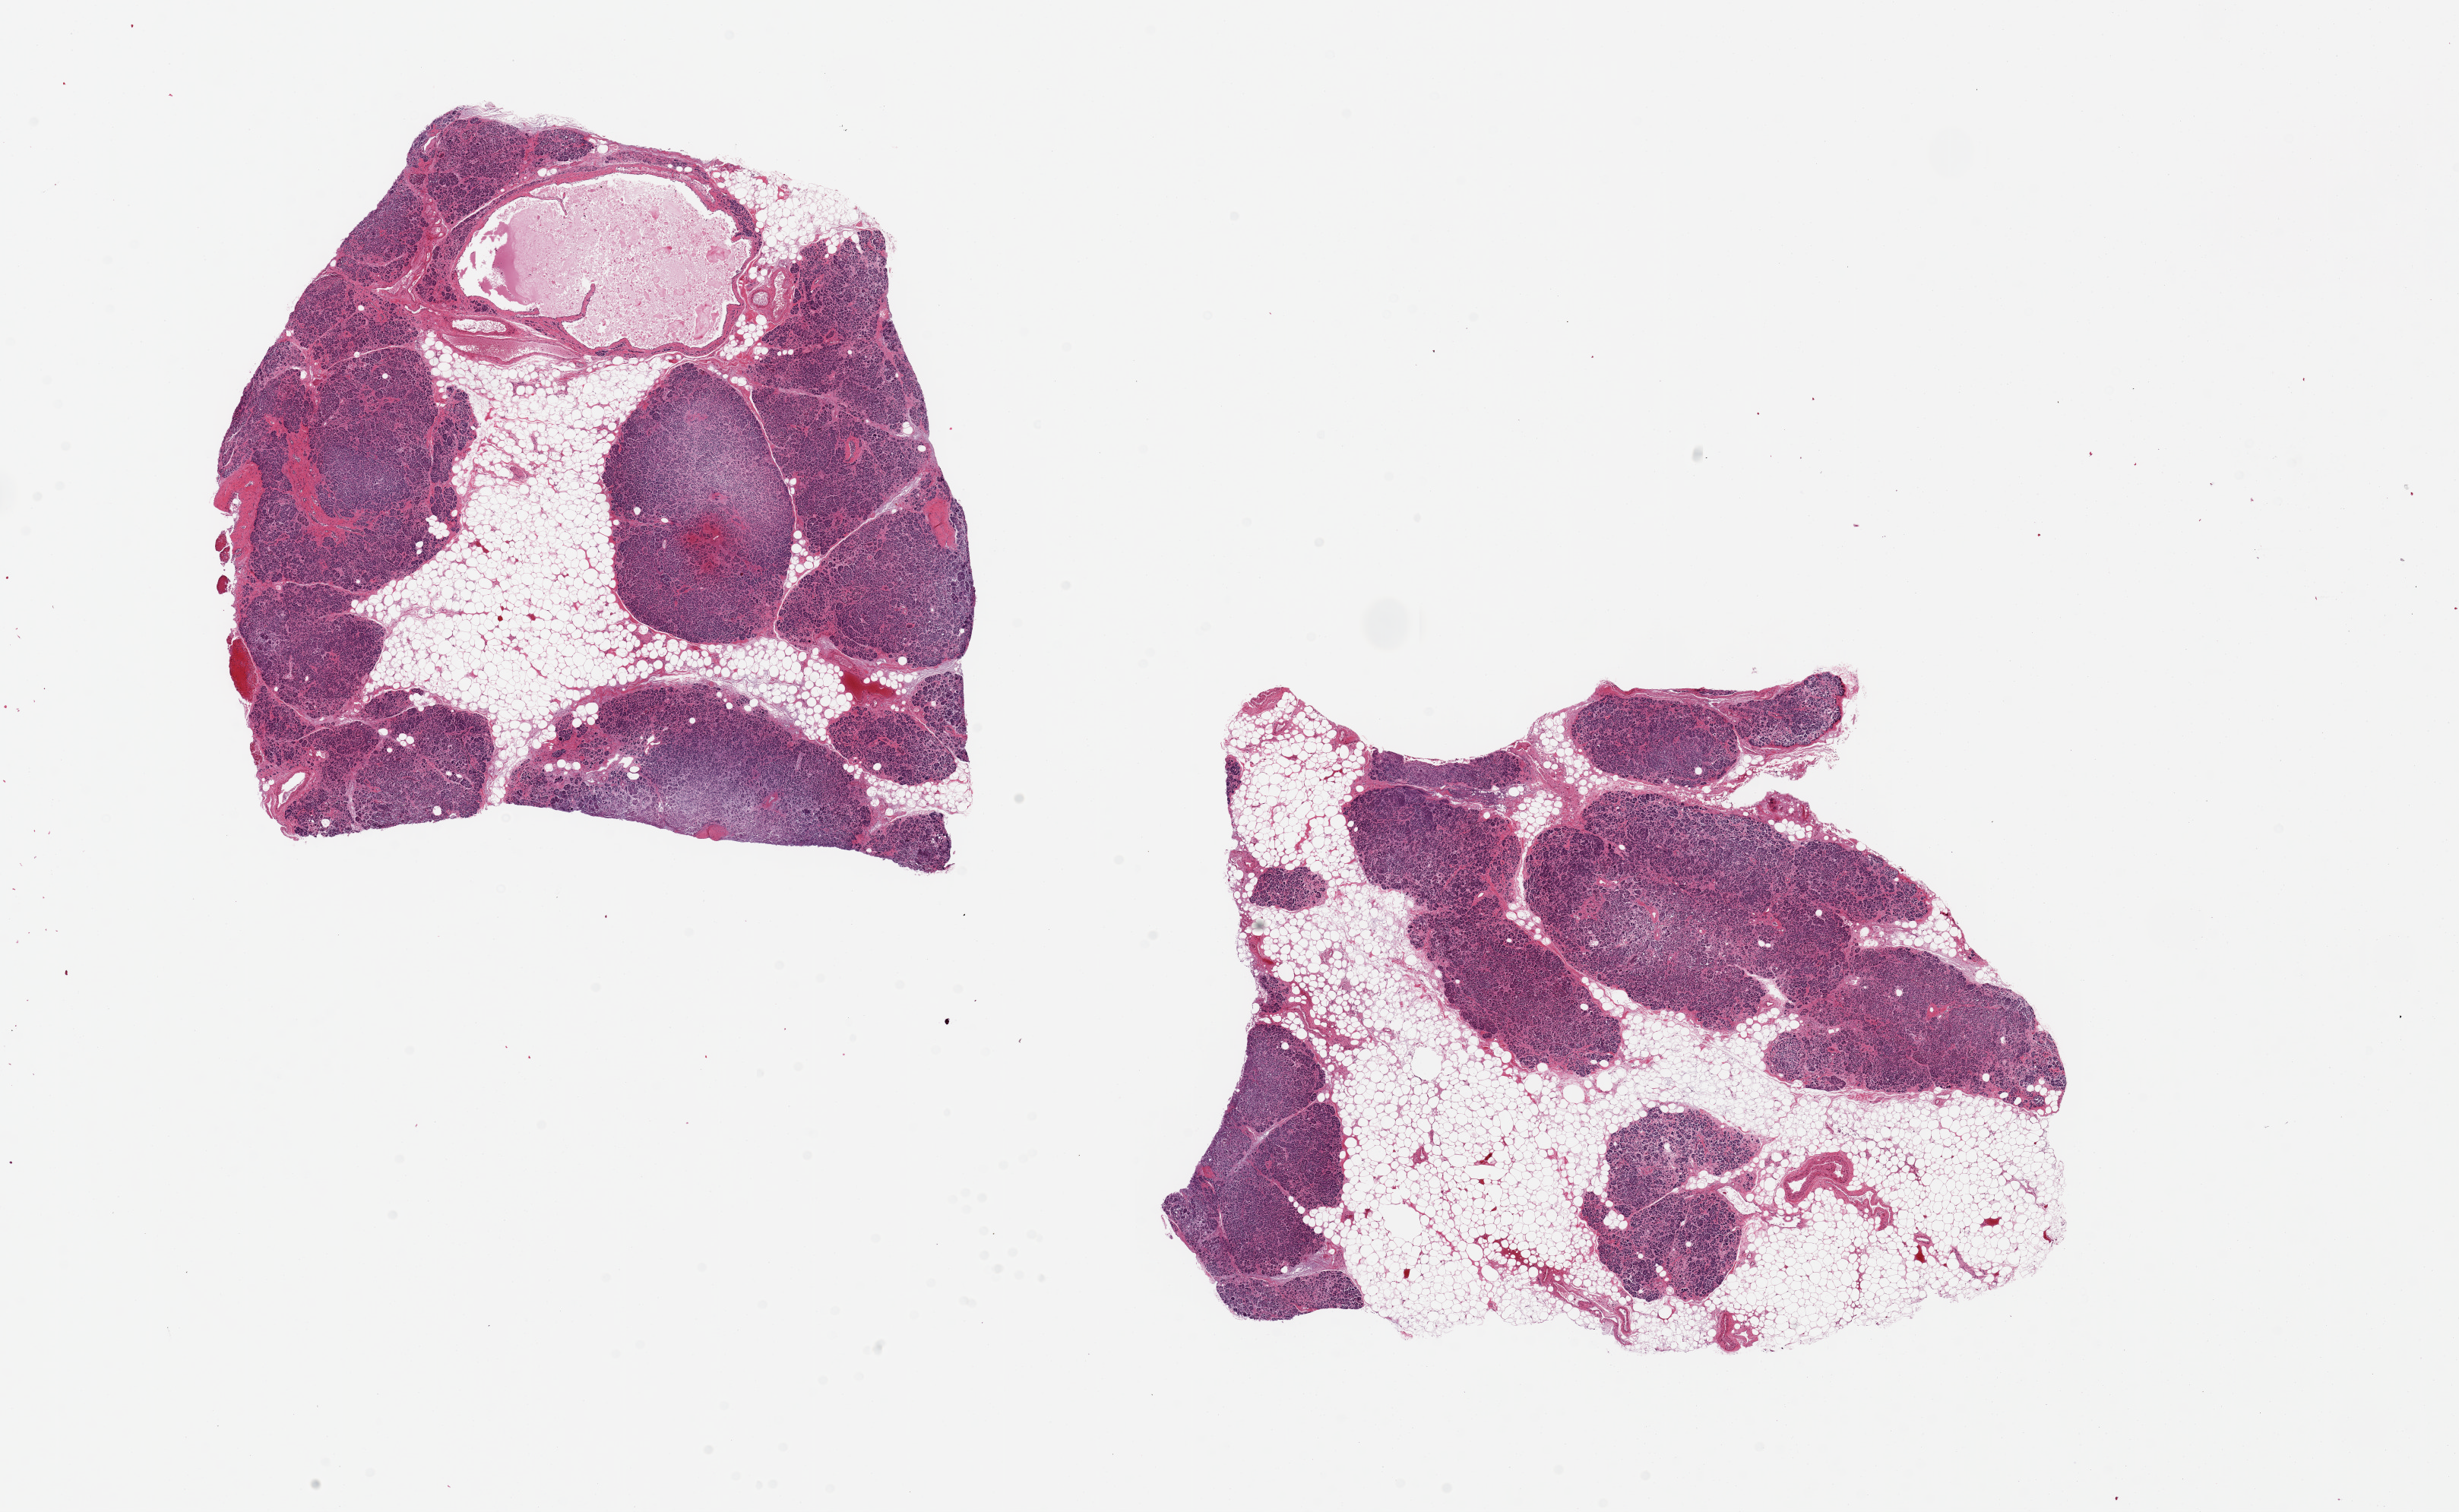
Digitized haematoxylin and eosin-stained section, low-resolution overview of the scanned area, about 25.6 x 15.7 mm. PAXgene-fixed paraffin-embedded (PFPE) section. Sampled site (target tissue): pancreas. Donor tissue sample. Donor: male.
Pathologist's review note for this sample: 2 pieces, 8x8 & 9x7mm; ~50% parenchyma, badly autolyzed/saponified; rest is intermingled fat.